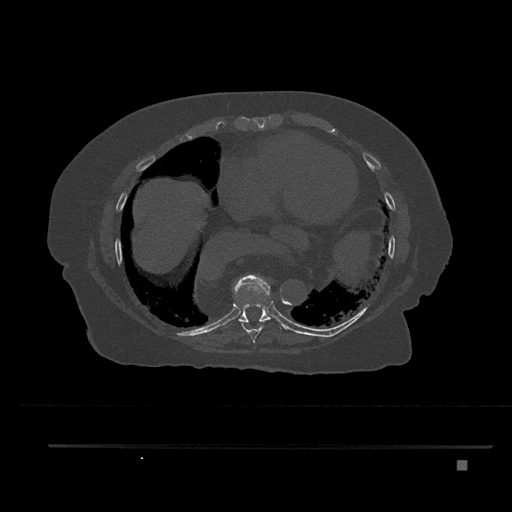
CT including the spine, one axial slice; reconstruction kernel Br40s/3; 120 kVp; bone window (W 1800 / L 400 HU); 512 × 512 image matrix. Patient: female, 76 years. From the clinical record (not read from this slice): primary cancer: lung.
Annotated regions visible in this slice (semi-automatically segmented with operator editing):
- T8 vertebra: bounding box (x1, y1, x2, y2) in pixels: (238, 290, 270, 346)
- T9 vertebra: (223, 274, 272, 327)